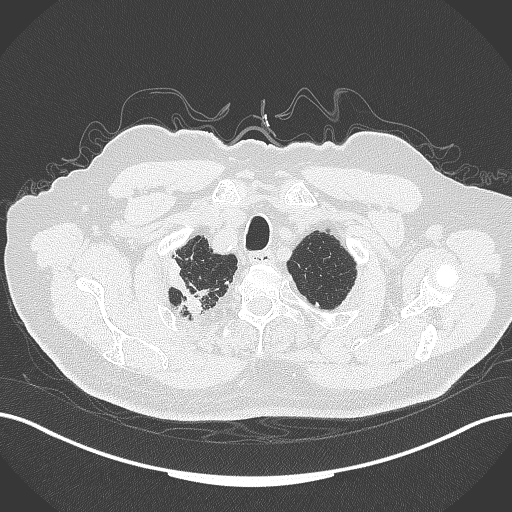
Chest CT, one axial slice; slice 328 of 389 in the series (ordered by position); 120 kVp; lung window (W 1500 / L -600 HU); 1 mm slice thickness; 512 × 512 image matrix. Male patient, age 72 years. Case-level facts recorded for this patient, not image findings: clinical TNM (as recorded): T1a N0 M0.
Annotated regions visible in this slice (rectangle marked by the reading radiologist):
- lung tumour (recorded histology: squamous cell carcinoma): bounding box <162,256,210,319> (left, top, right, bottom; pixels)